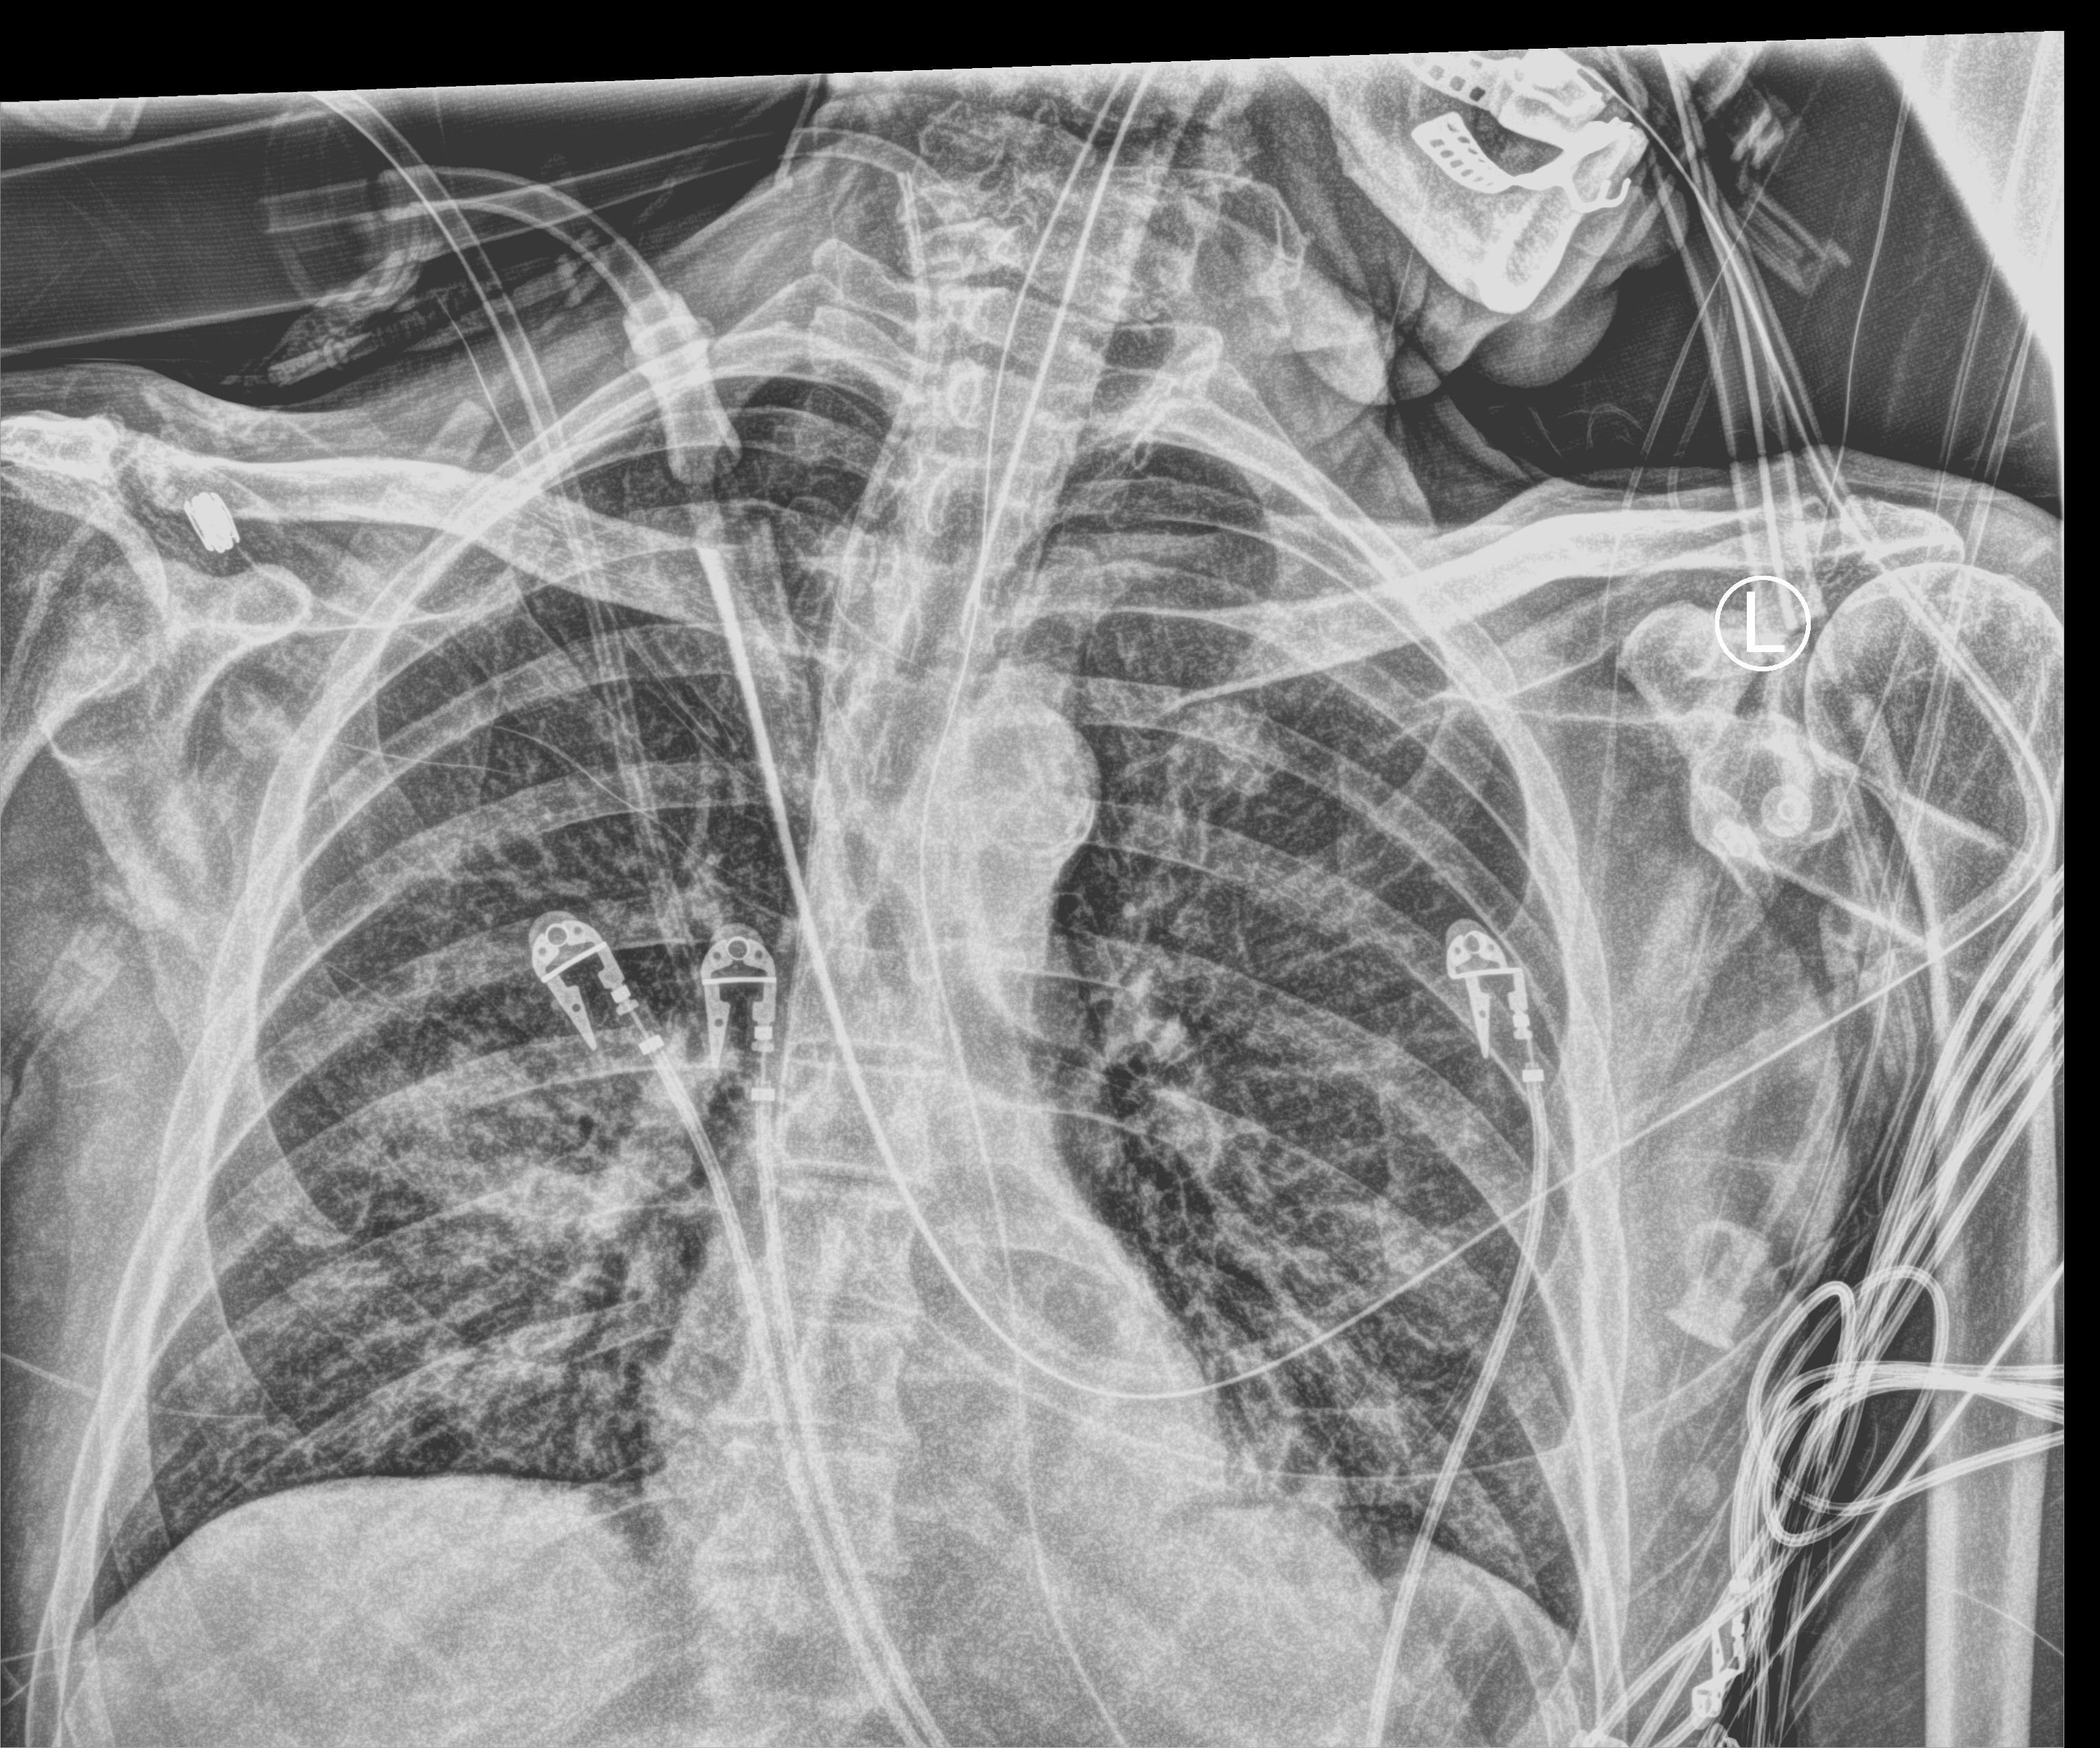
Portable chest radiograph, anteroposterior (AP) projection. Male patient hospitalised with COVID-19, age 75–90 years.
Admission-level facts for this patient (not findings on this image; timing relative to this image not recorded):
- smoking status (admission record): former